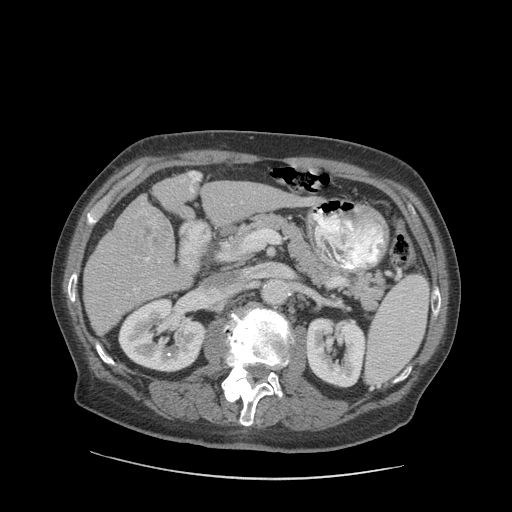
Contrast-enhanced abdominal CT (liver protocol), one axial slice; position 42 of 89 along the scan axis; 140 kVp; soft-tissue window (W 400 / L 40 HU); 2.5 mm slice thickness; 512 × 512 image matrix, field of view 420 × 420 mm. Case-level facts recorded for this patient, not image findings: diagnosis: hepatocellular carcinoma (patient treated with transarterial chemoembolisation; whether this scan precedes or follows treatment is not stated here); TNM stage (as recorded): Stage-I; Child-Pugh class: A.
Structures marked on this image (semi-automatically segmented with operator editing):
- liver parenchyma outside the tumour (the mass and vessels are separate outlines, so this box may not span the whole liver): box from (x=84, y=171) to (x=296, y=334) px
- mass: (x=123, y=207)–(x=172, y=265)
- liver vessels: (x=127, y=172)–(x=243, y=296)